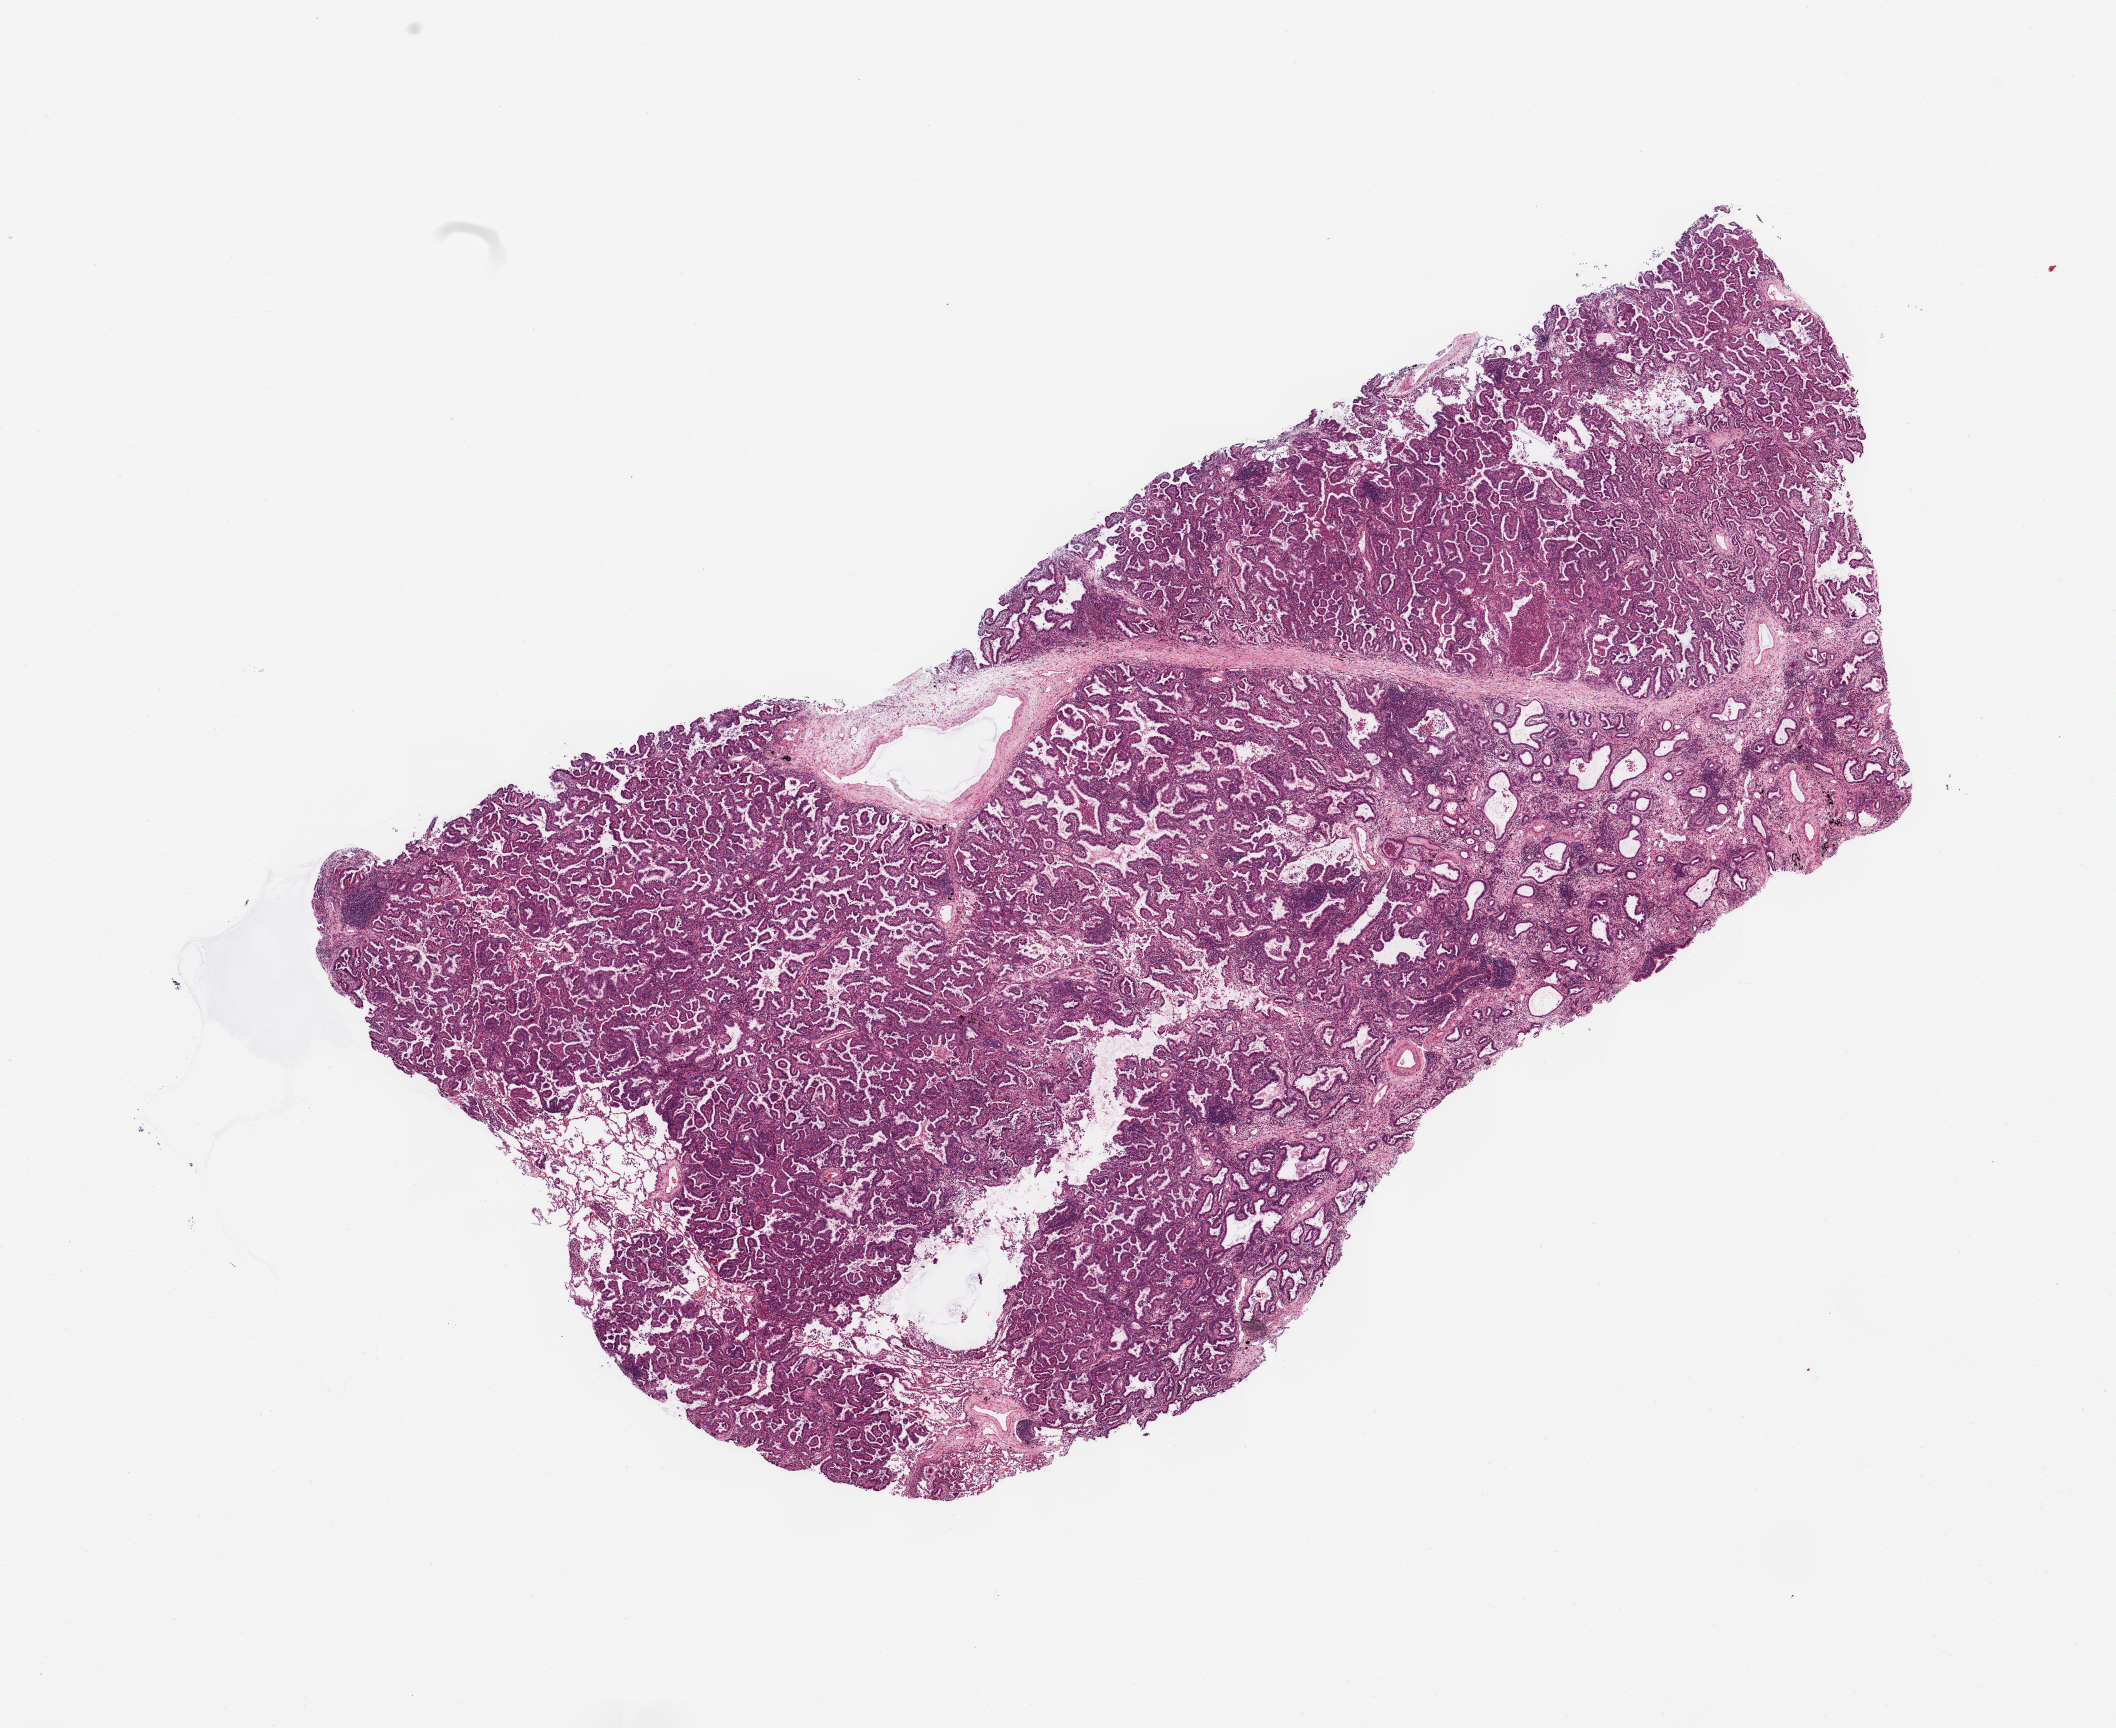
Digitized H&E tissue section (whole slide), shown as a low-resolution overview of the whole scanned area (about 16.7 x 13.7 mm). Tumour tissue sample, sampled site: lung. Patient: female, age 58 years. Histologic grade: G2 (moderately differentiated). Pathologist review of this section (percent, as recorded): tumour nuclei 90%, necrosis 2%.
AJCC pathologic stage: IIA. Histologic diagnosis: Adenocarcinoma, NOS. Primary tumour site (as recorded): right lower lobe.